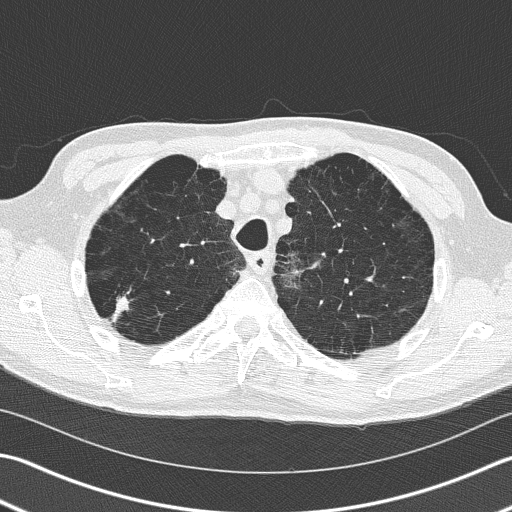
Low-dose screening chest CT, axial slice. Baseline annual screen. Lung window (W 1500 / L -600 HU). 2 mm slice thickness. Lung (sharp) reconstruction kernel (B50f). Slice 38 of 163 in the series. 512 × 512 image matrix. Male, age 66 years at enrolment.
• Expert reader's lesion annotation, bounding box <90,274,147,339> (left, top, right, bottom; pixels).
• Screening reader's record for this exam (one nodule recorded; not confirmed to be the boxed lesion): non-calcified nodule or mass ≥4 mm, right upper lobe, 39 × 23 mm, spiculated (stellate) margins, soft tissue attenuation.
• Official screen result: positive, change unspecified: nodule(s) >= 4 mm or enlarging nodule(s), mass(es), or other non-specific abnormalities suspicious for lung cancer.
• Later outcome: lung cancer diagnosed 36 days after this screen — squamous cell carcinoma, NOS, right upper lobe, poorly differentiated (G3), stage IB (AJCC 6th edition), 23 mm at pathology.